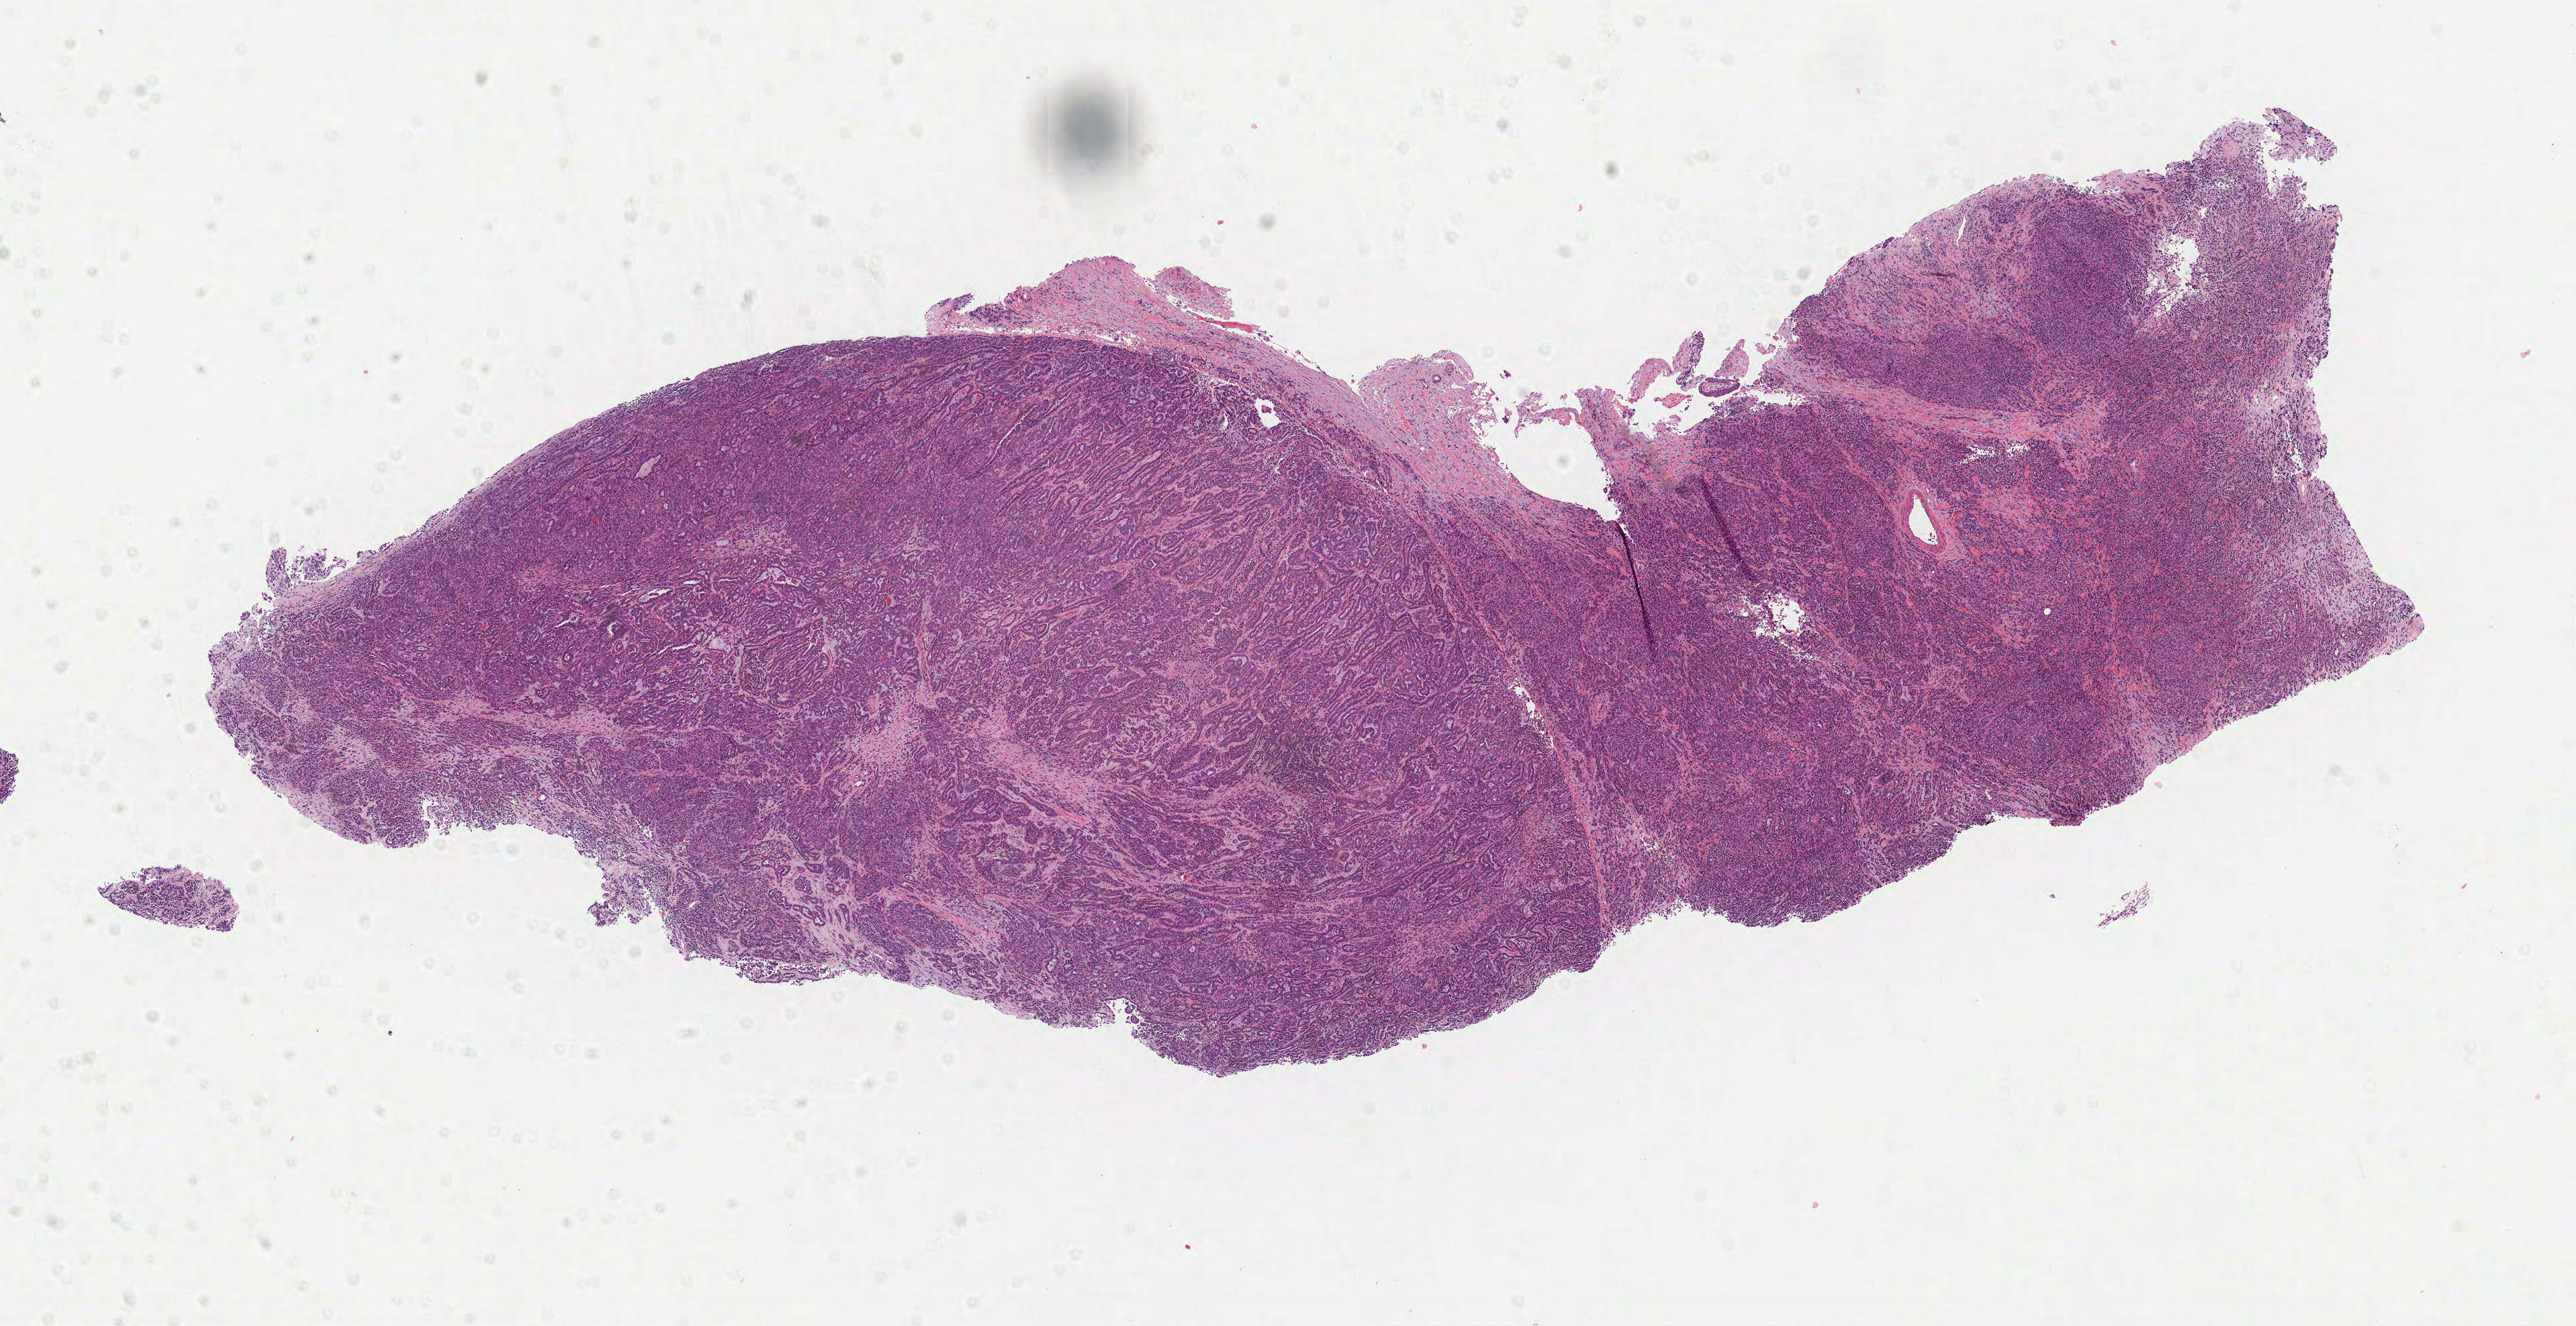
Digitized Hematoxylin and eosin (H&E) stained tissue section (whole slide), whole scanned area (about 15.5 x 8.0 mm, slide scanned at 40x) shown as a low-resolution overview, FFPE section, kidney, primary tumour sample. Female, age 28 years at initial diagnosis.
Laterality: right. AJCC pathologic stage: III (7th edition). TNM: T3 N1 MX. Pathologic diagnosis: Papillary adenocarcinoma, NOS.